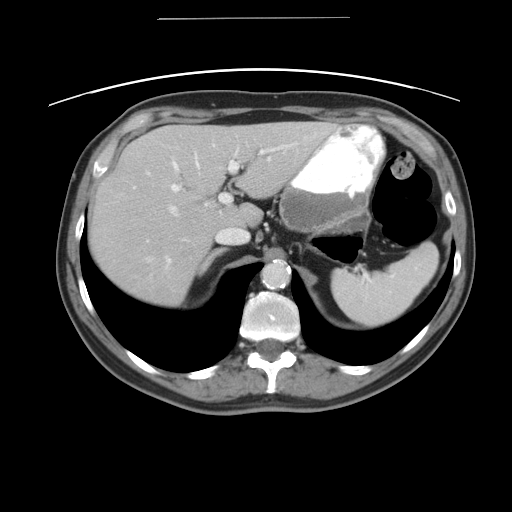
Contrast-enhanced abdominal CT, one axial slice; position 33 of 49 along the scan axis; reconstruction kernel STANDARD; intravenous contrast given; soft-tissue window (W 400 / L 40 HU); 512 × 512 image matrix, field of view 413 × 413 mm. Male patient, age 57 years. From the clinical record (not read from this slice): diagnosis: colorectal cancer liver metastases, imaged before liver resection; multiple liver metastases: yes; largest metastasis: 4 cm; disease in both lobes: no.
Annotated regions visible in this slice (manually delineated by an expert):
- hepatic veins: bounding box (x1, y1, x2, y2) in pixels: (145, 157, 269, 260)
- liver: (89, 121, 334, 305)
- planned liver remnant (the part of the liver to remain after resection): (208, 121, 334, 229)
- portal vein (with intrahepatic branches): (132, 141, 297, 260)